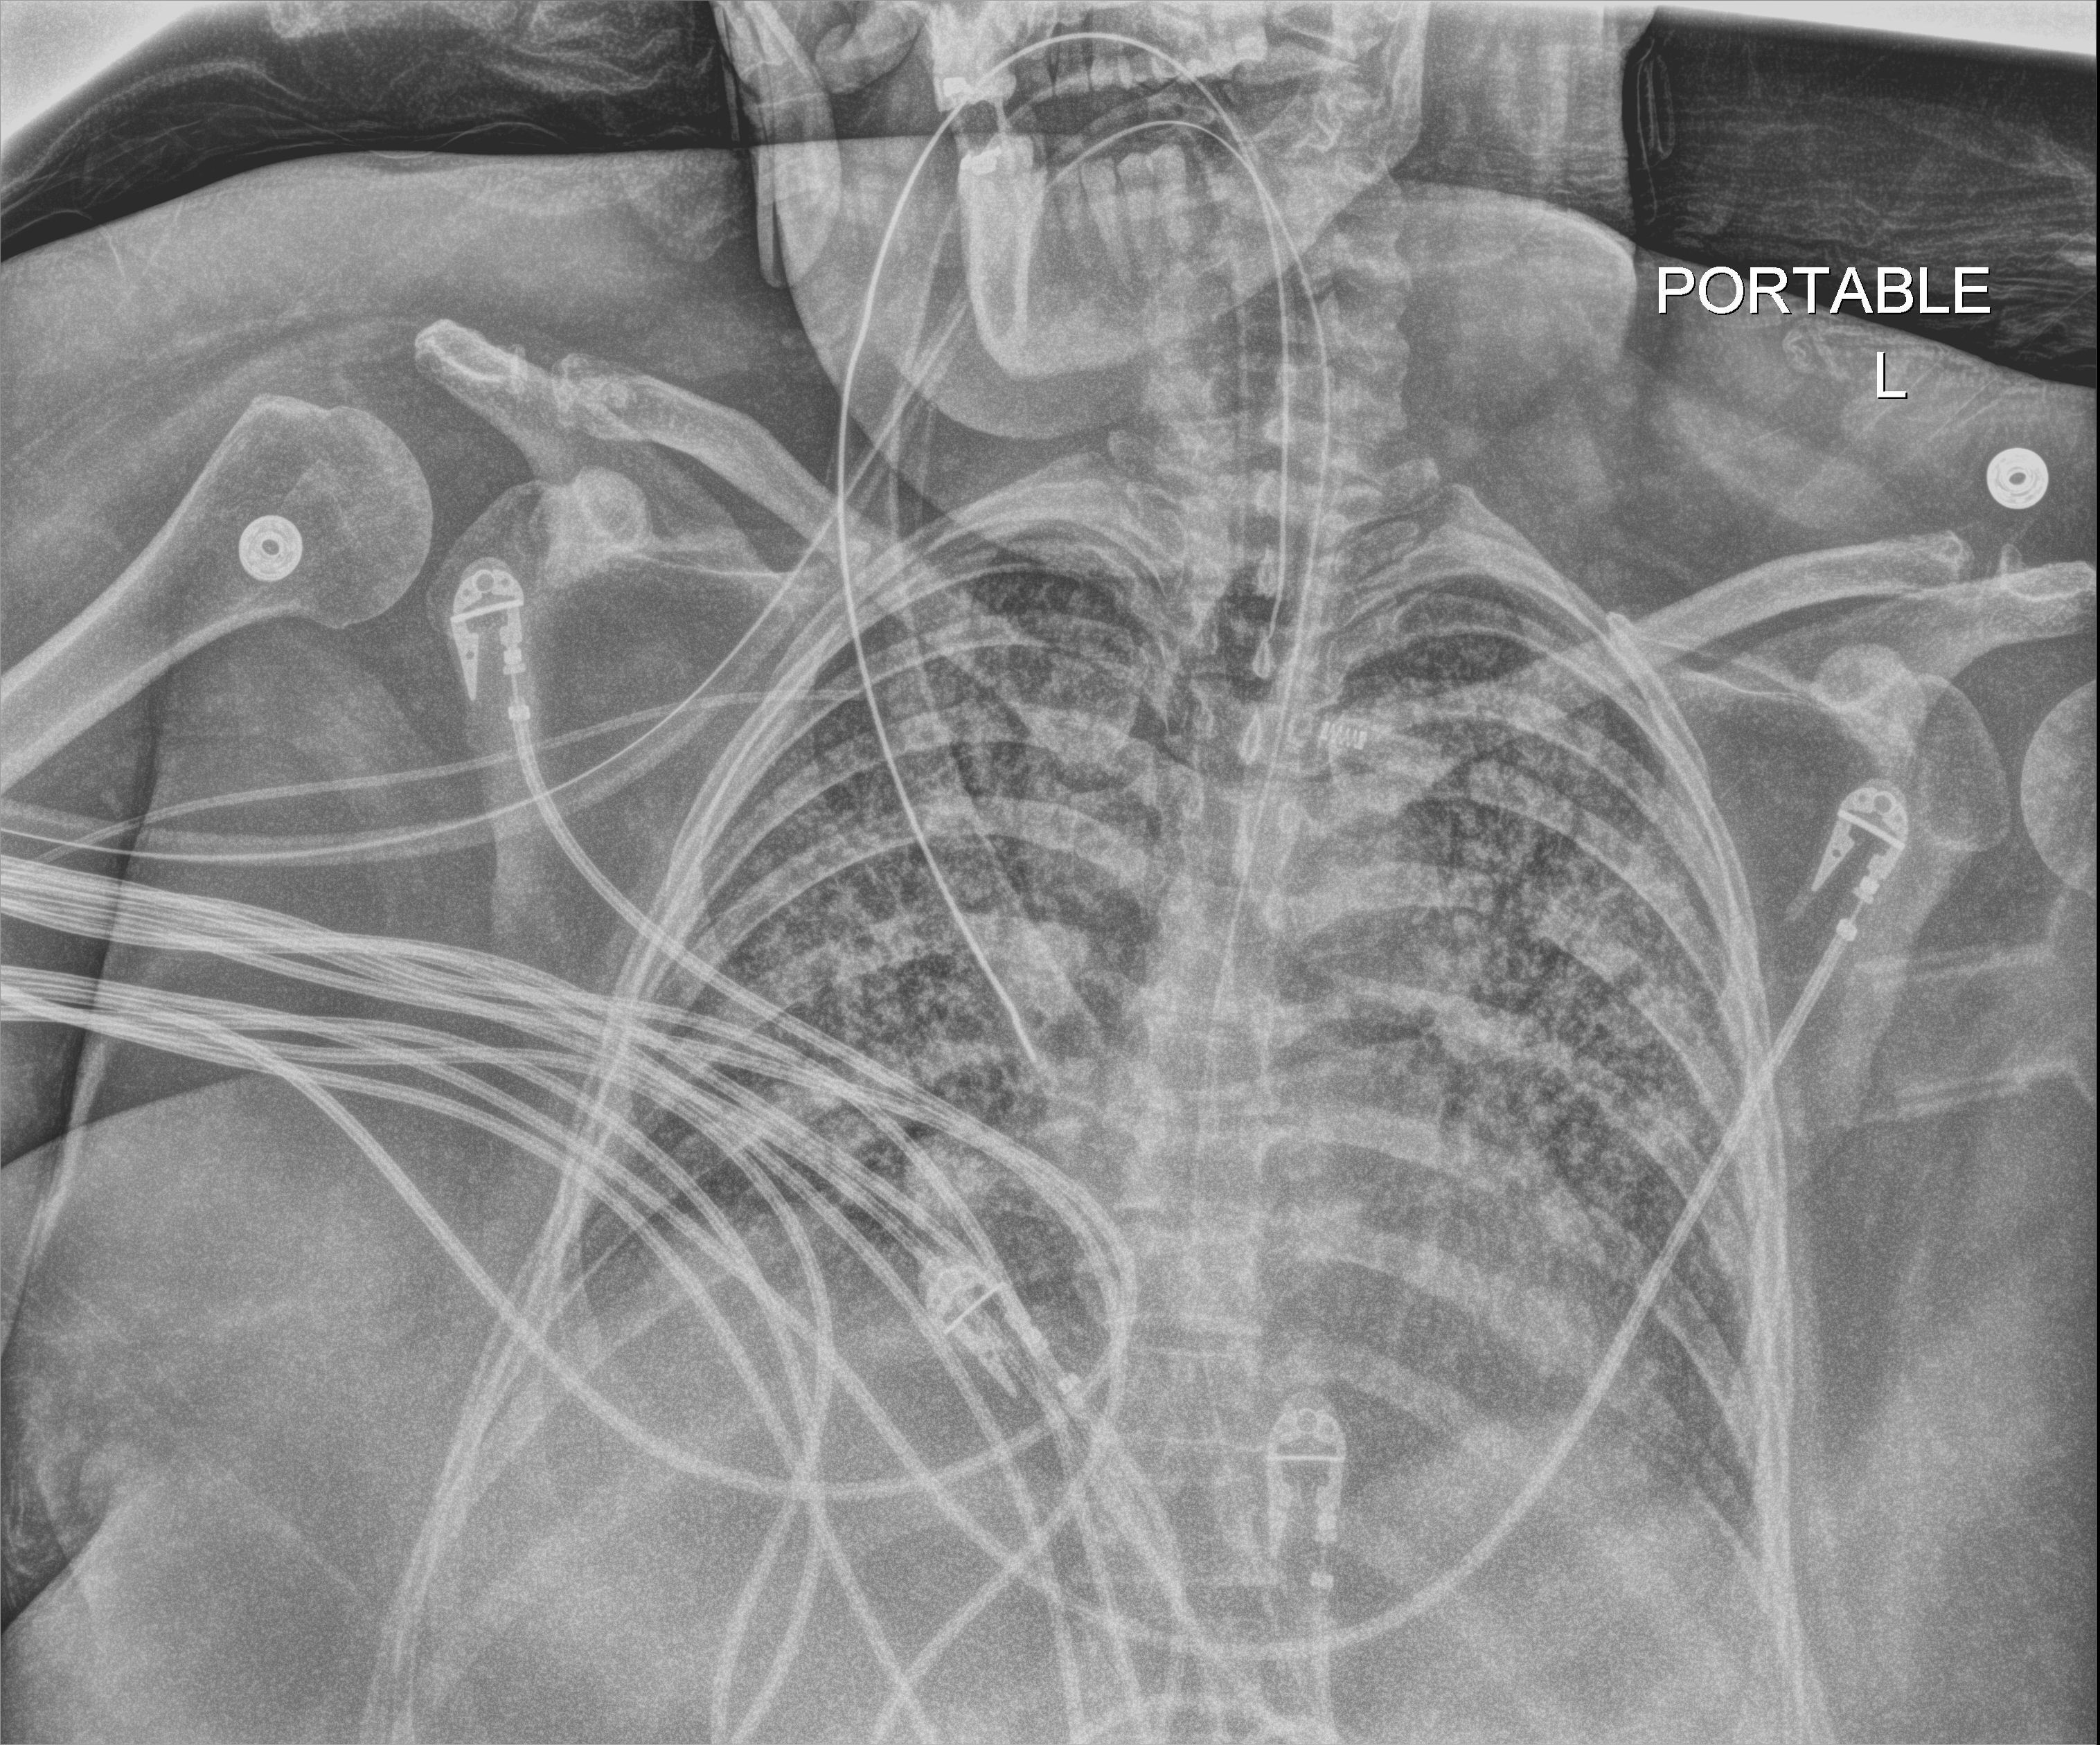
Chest radiograph (digital radiography); anteroposterior (AP) projection. Female patient hospitalised with COVID-19, age 18–59 years.
Hospital-stay facts (about this admission, not read from this image; timing relative to this image not recorded): mechanically ventilated during this hospital stay: yes; length of hospital stay: 95 days; admitted to intensive care during this hospital stay: yes.